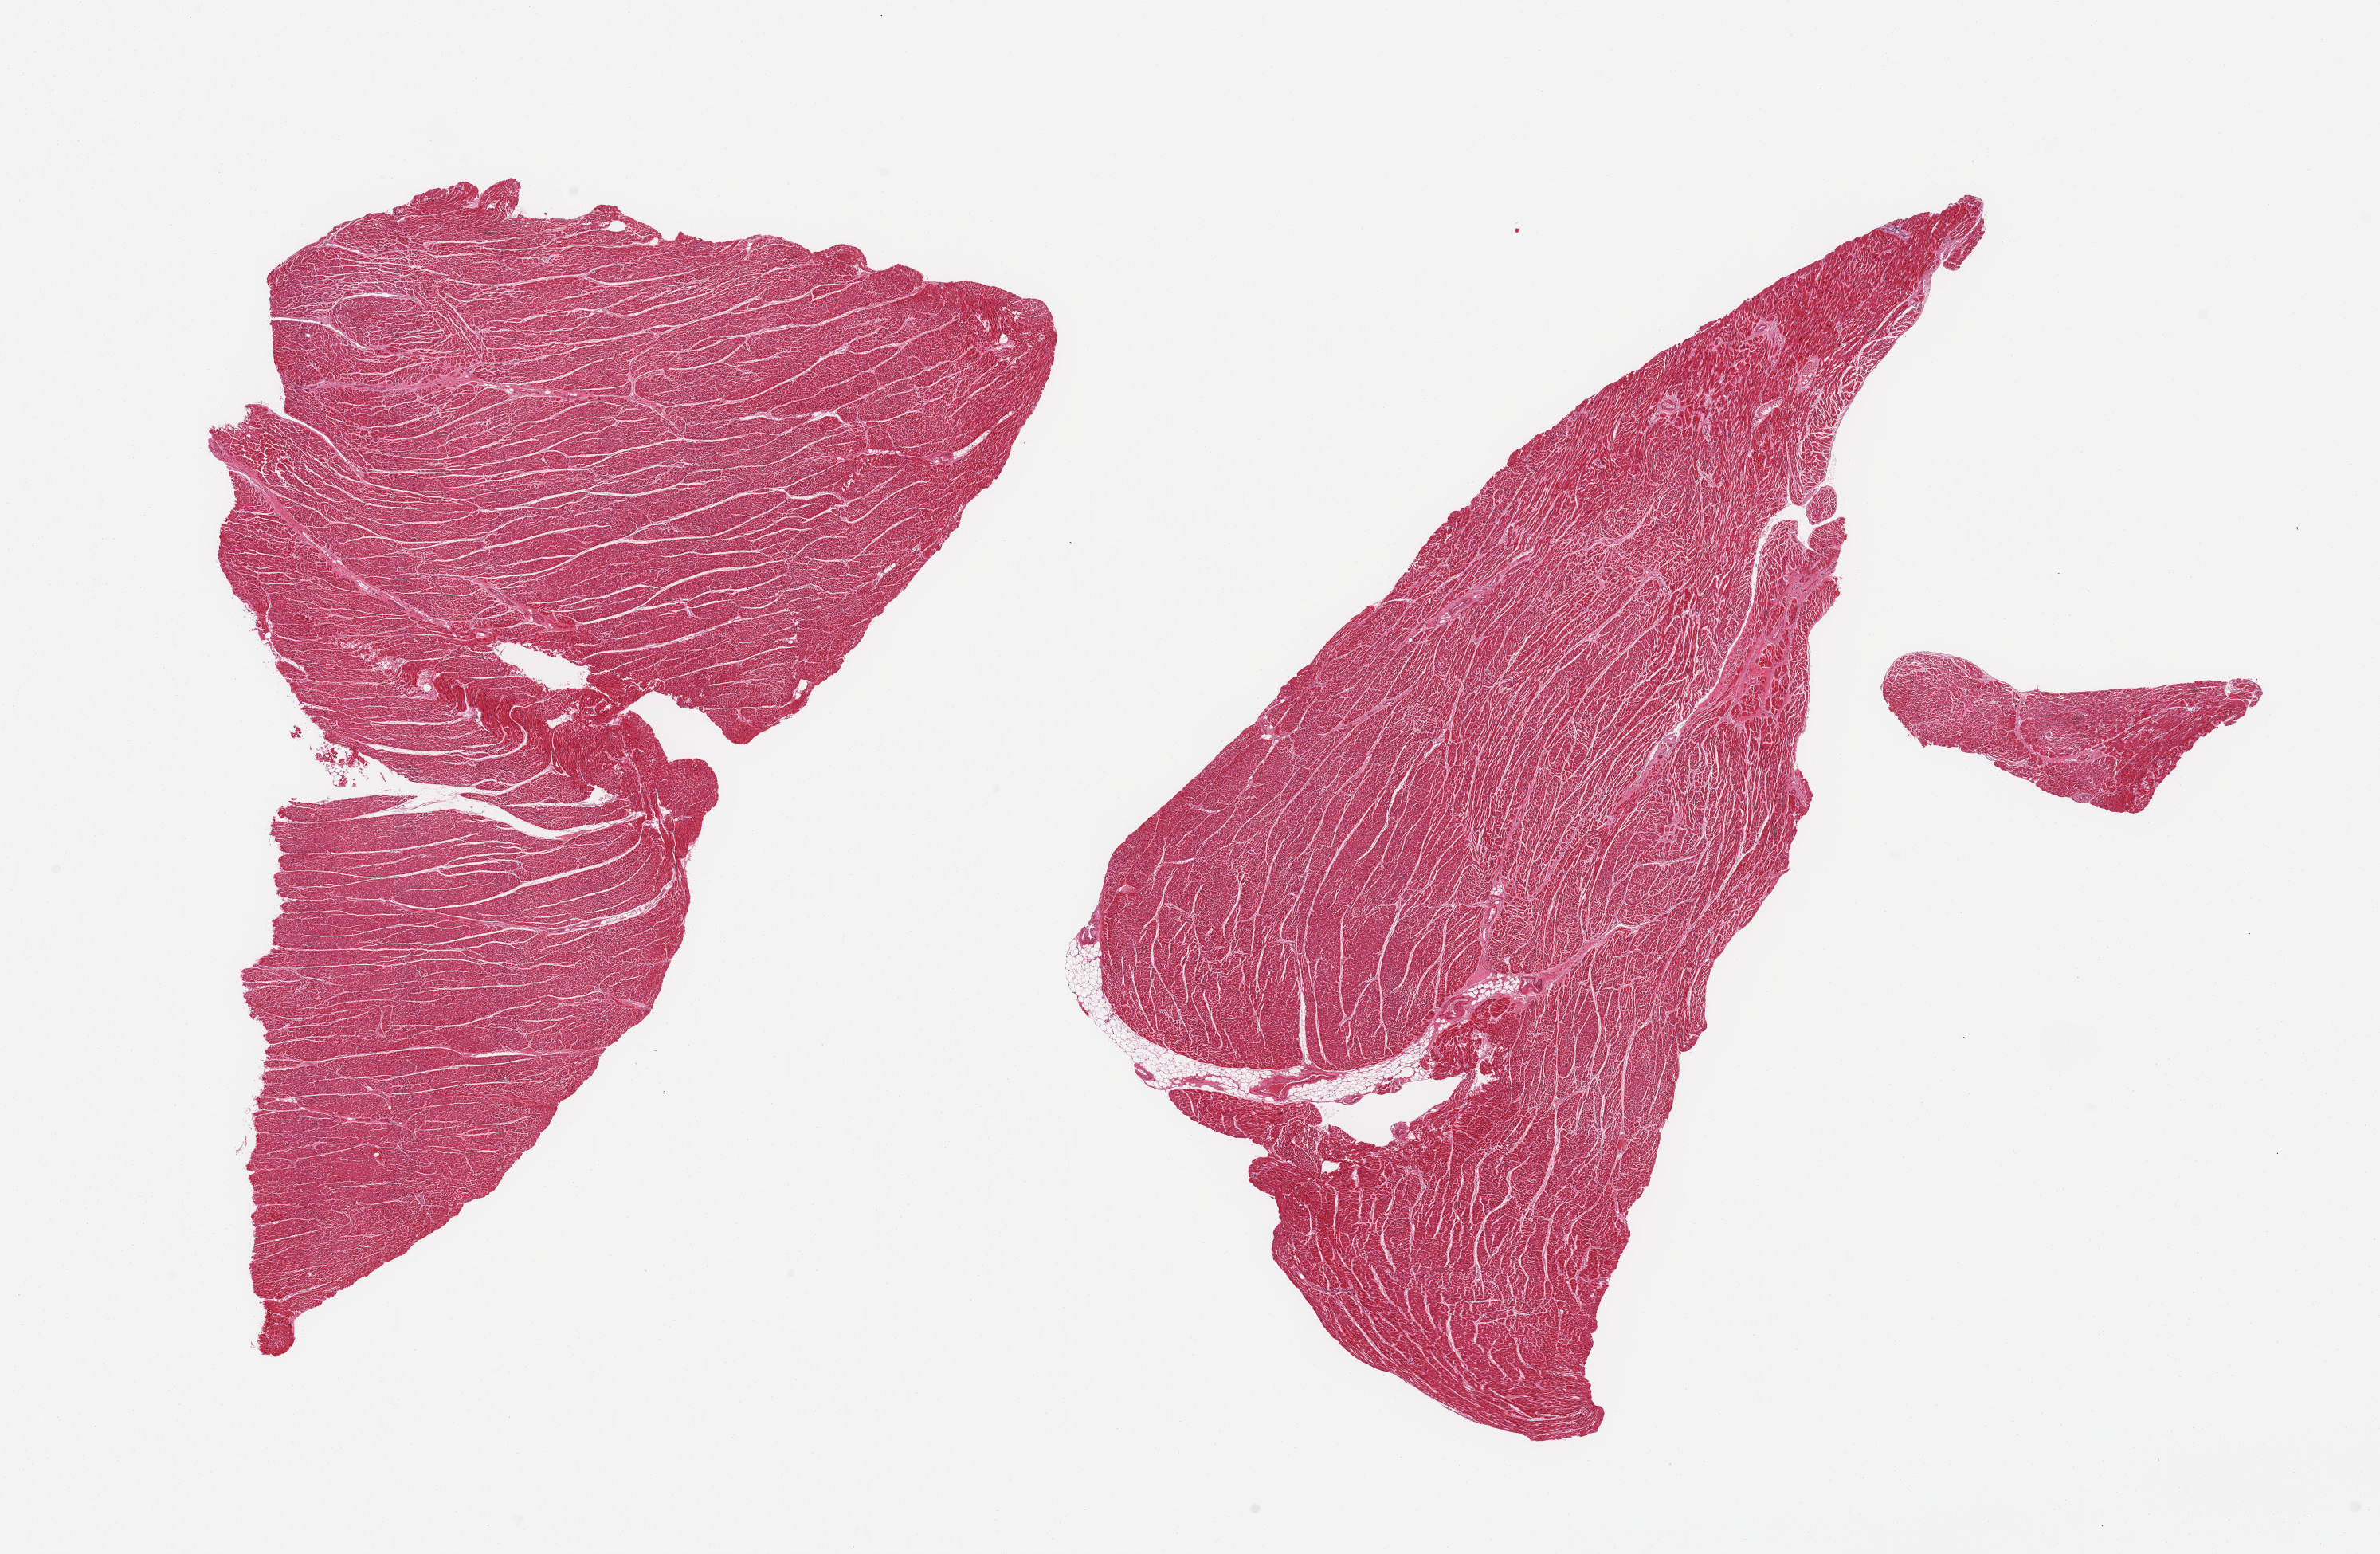
H&E whole-slide image, brightfield — whole scanned area (about 23.6 x 15.4 mm, acquisition: 20x scan) shown as a low-resolution overview; PAXgene-fixed paraffin-embedded (PFPE) section; section of heart (target tissue); donor tissue sample. Donor: male.
Pathologist's review note for this sample: 2 pieces, mild-moderate chronic ischemic changes/interstitial fibrosis.